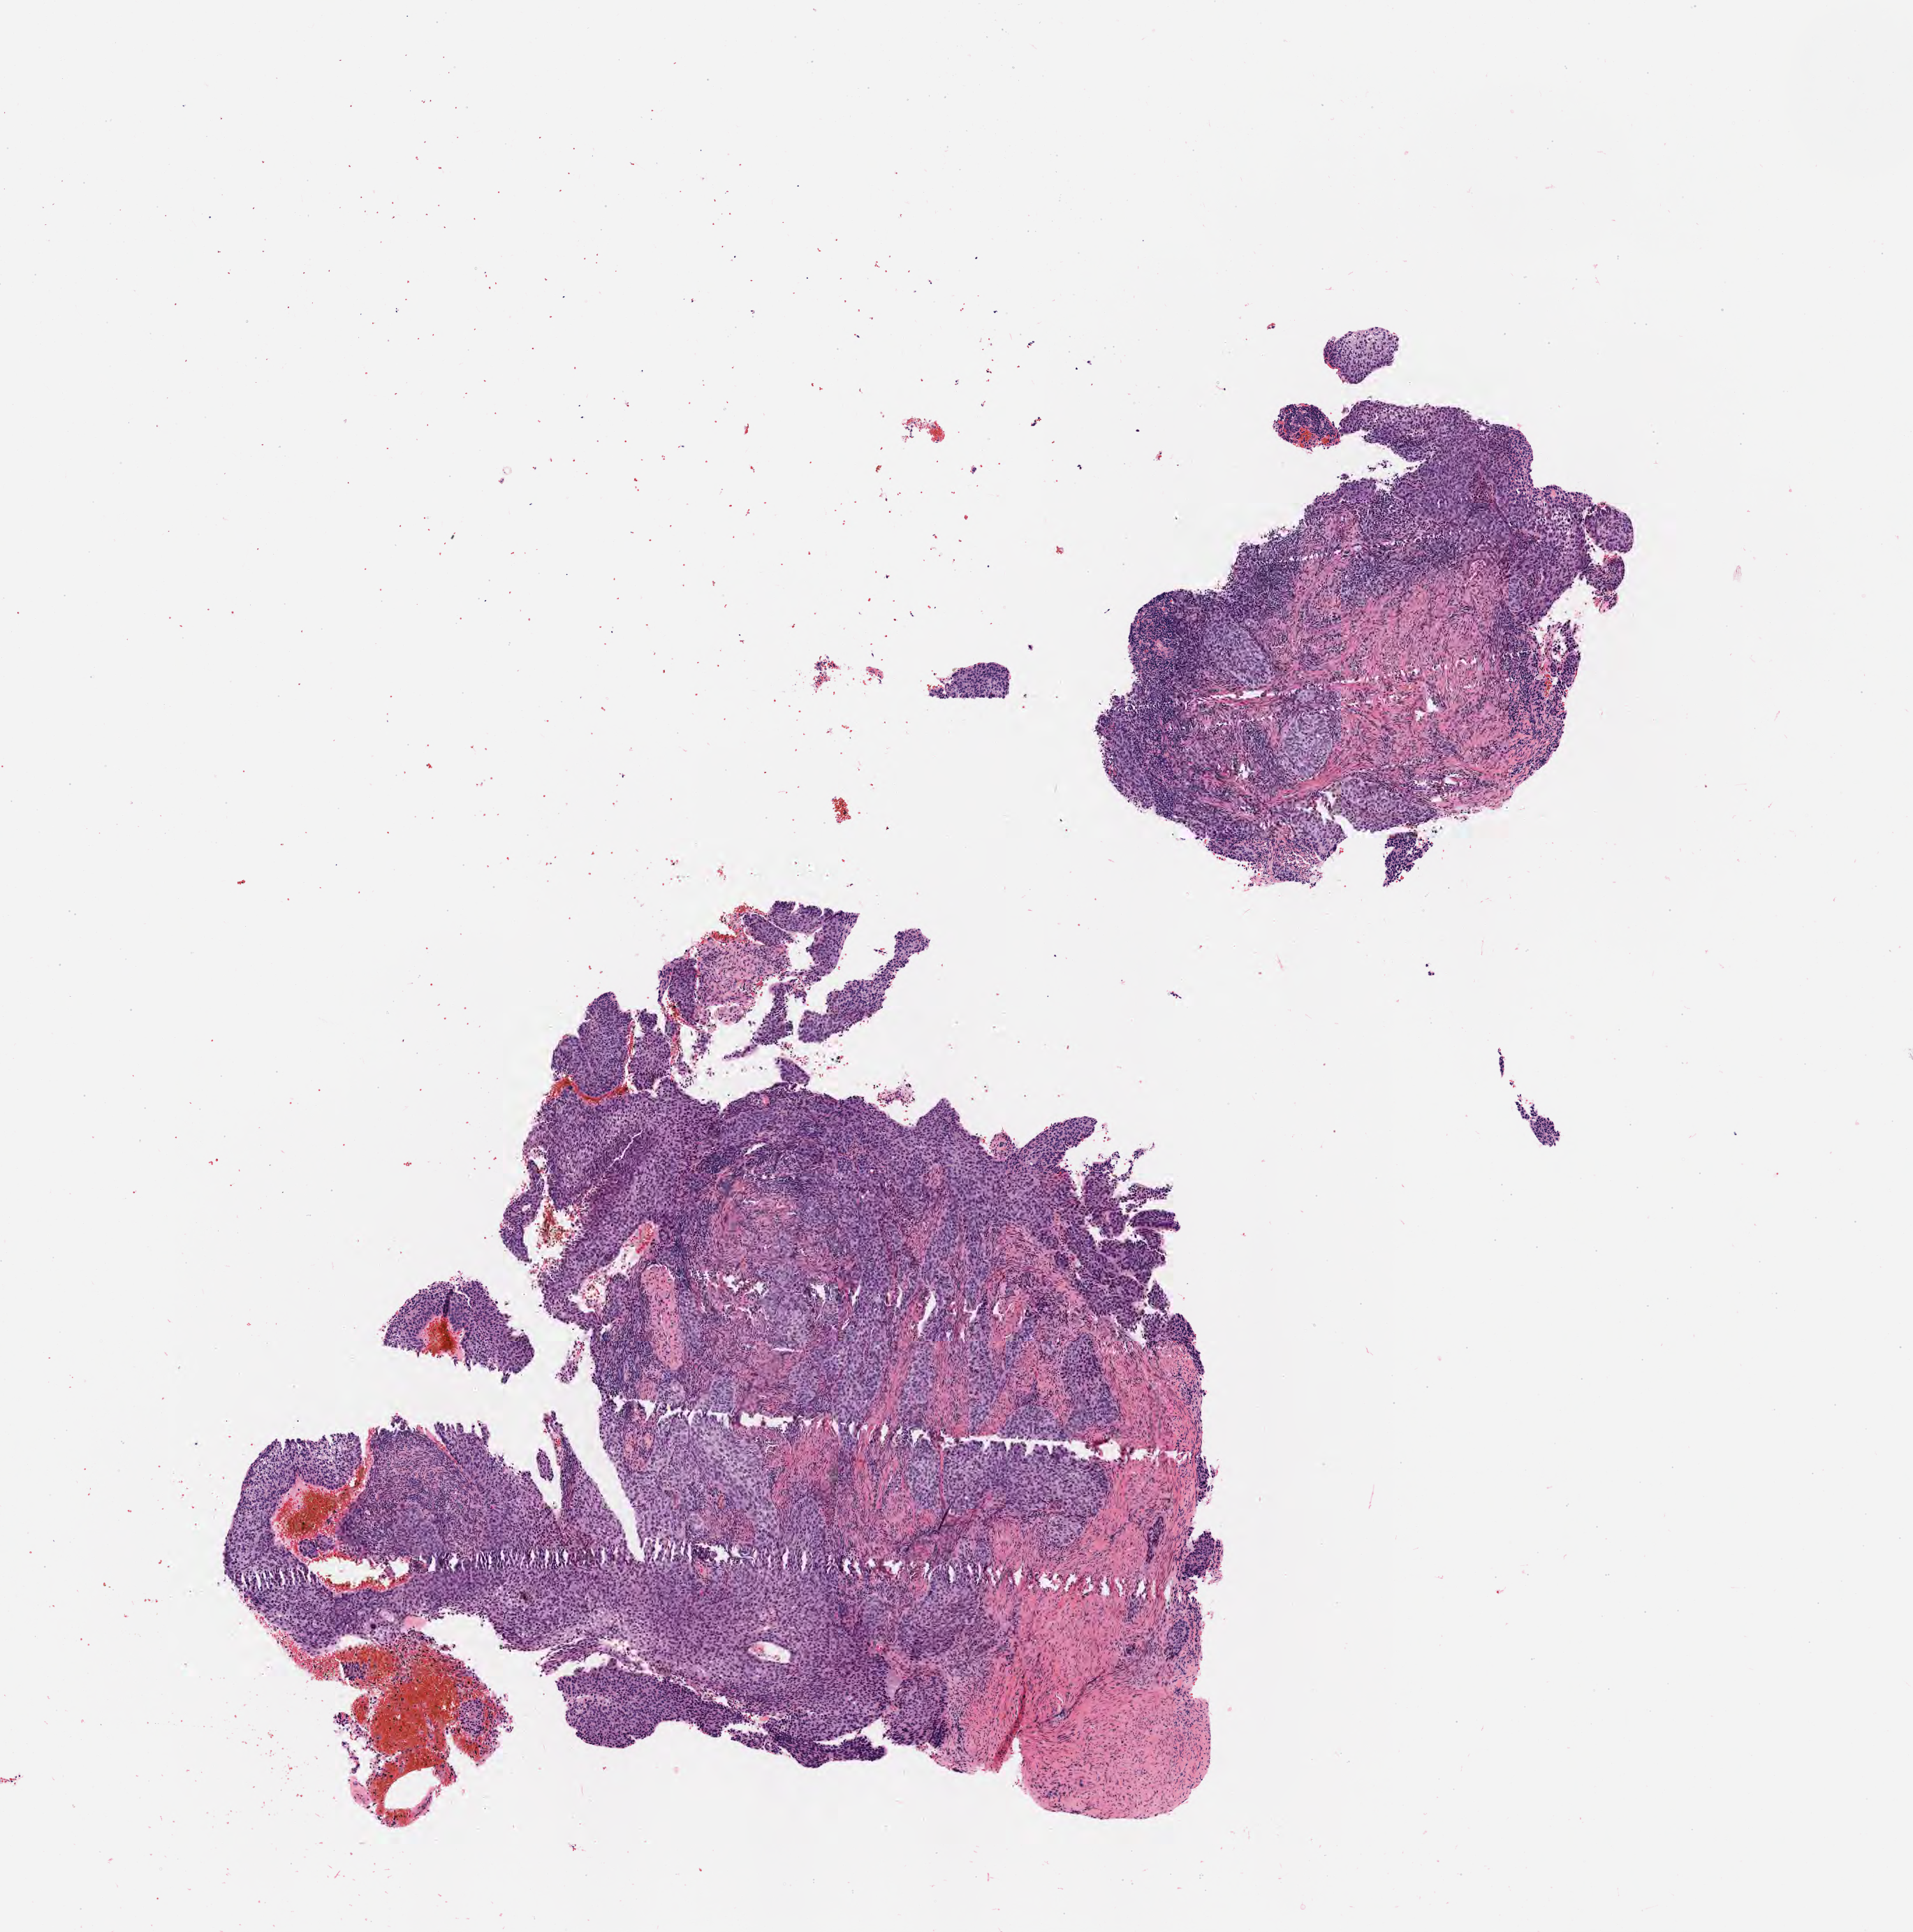
Digitized H&E-stained section — whole scanned area (about 5.5 x 5.6 mm) shown as a low-resolution overview, specimen: tumor tissue, anatomic site: cervix. Patient: female, 51 years old.
- diagnosis: Squamous cell carcinoma, large cell, nonkeratinizing, NOS